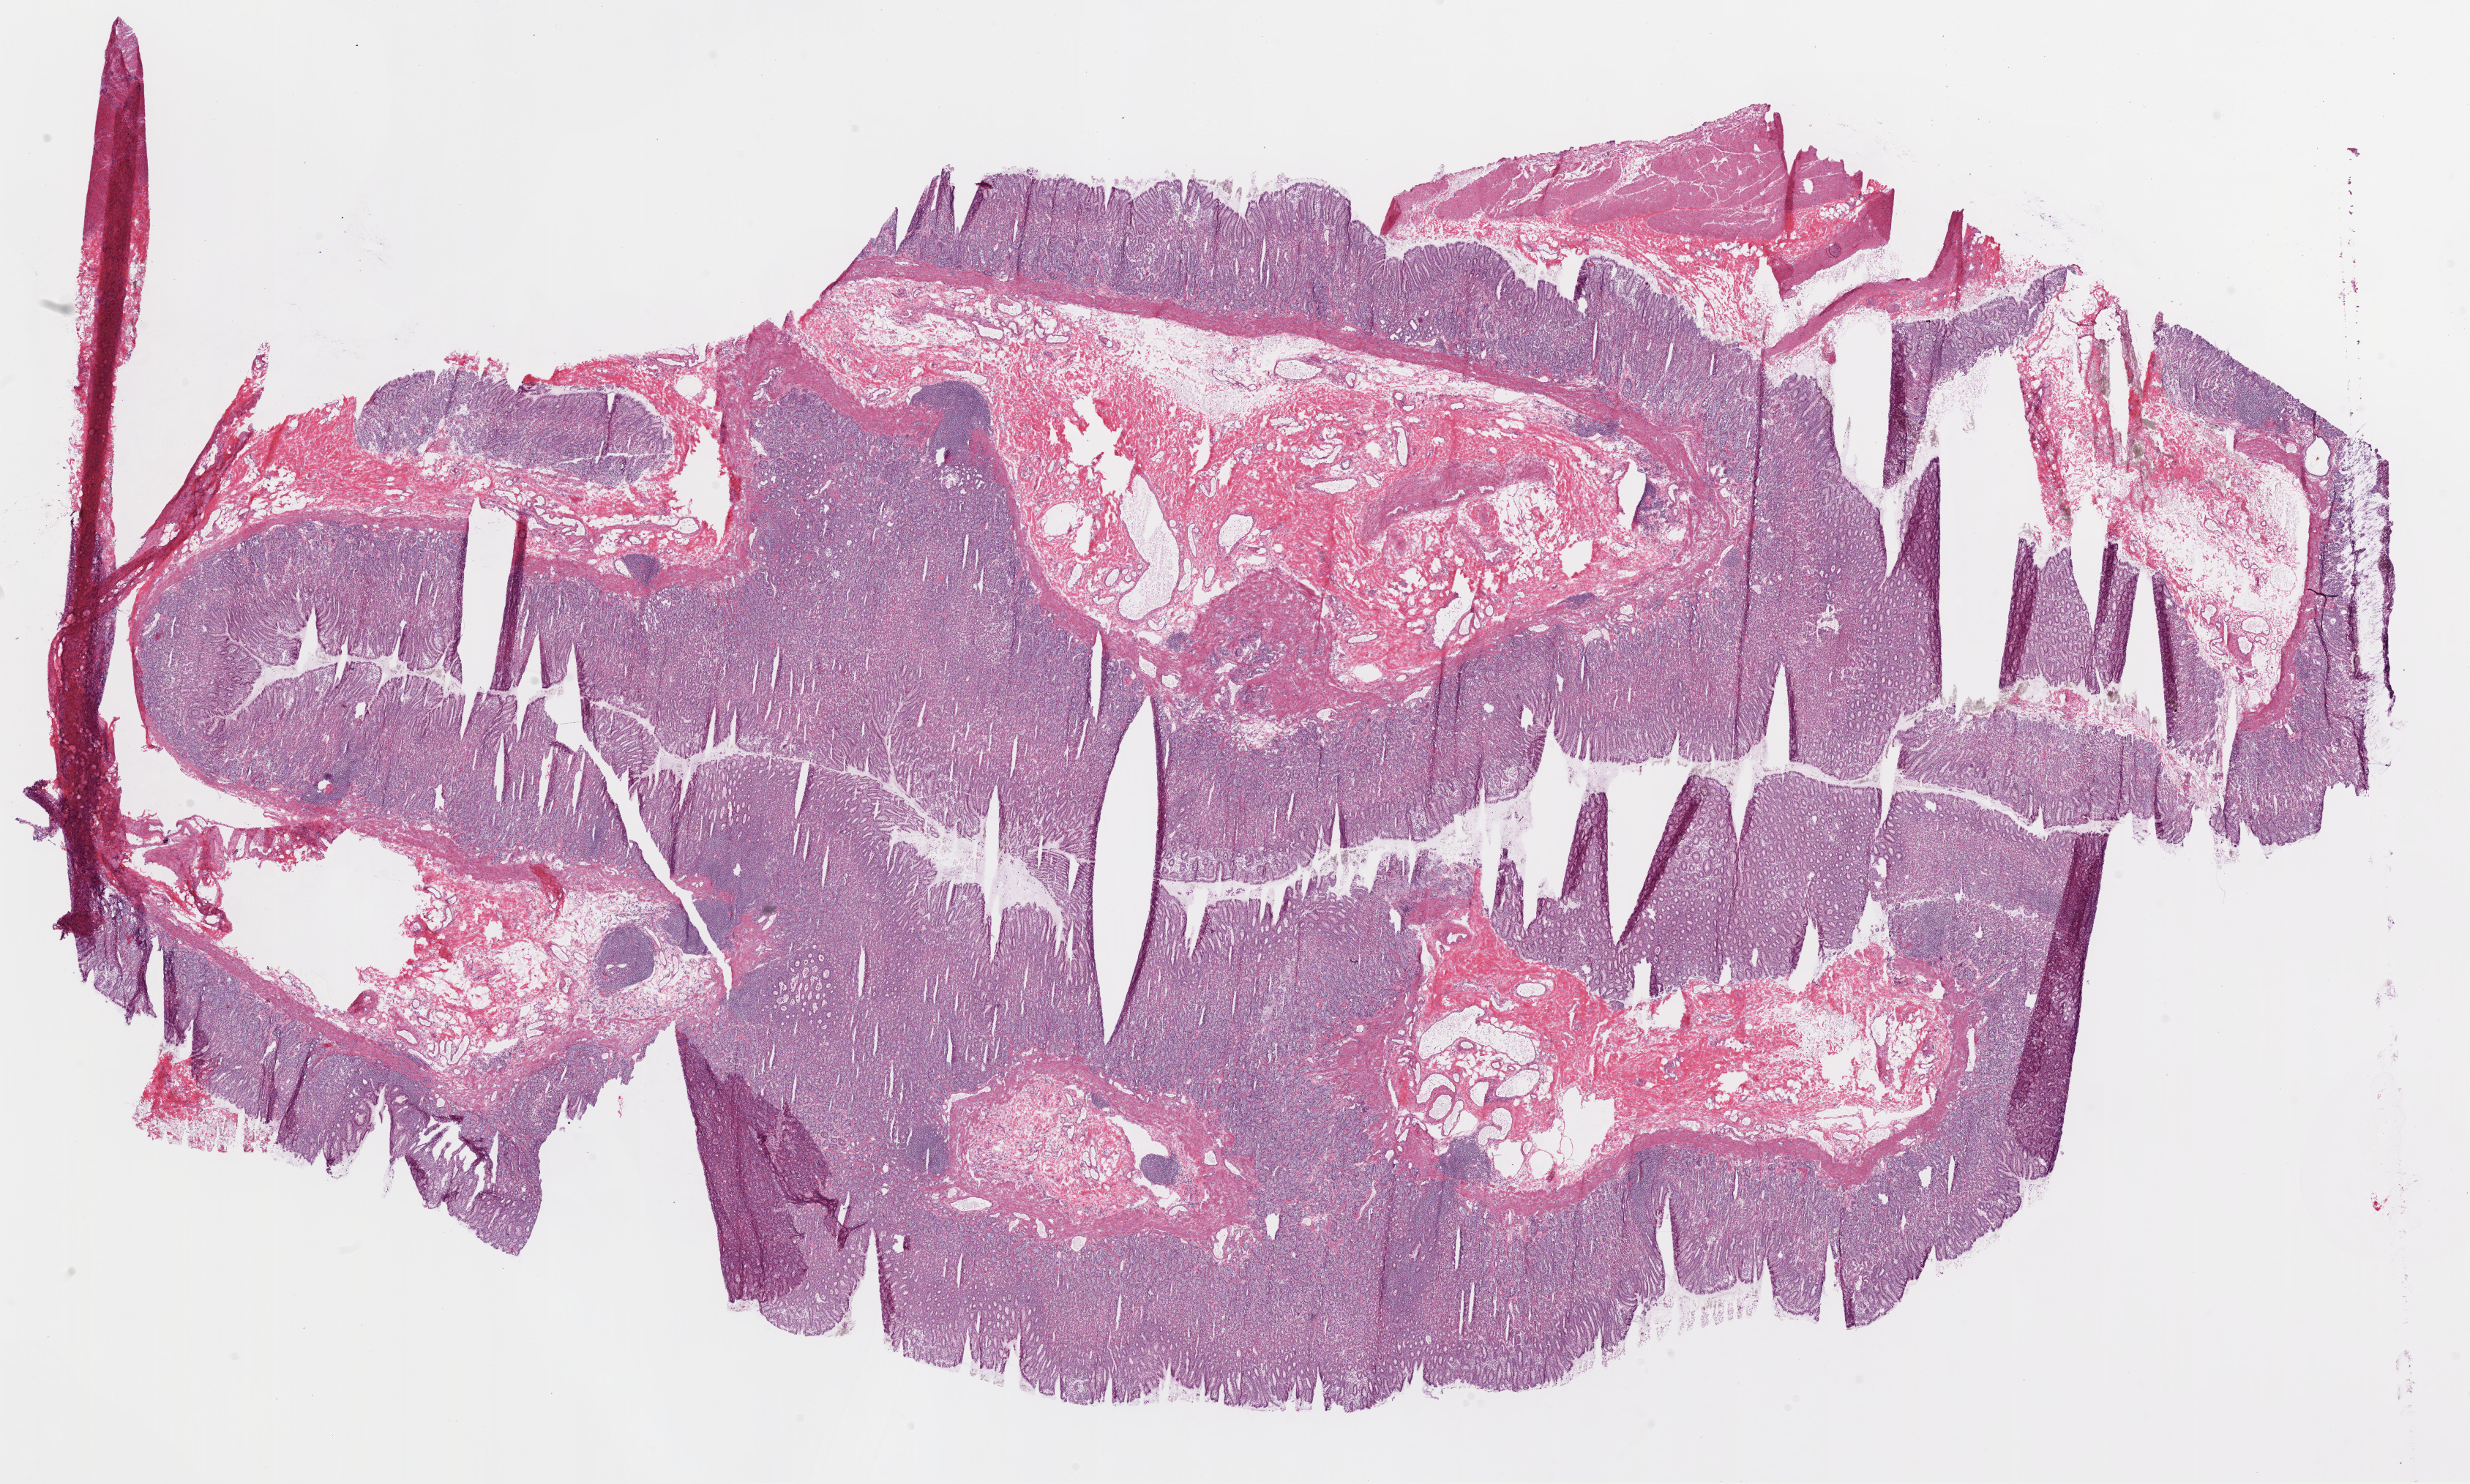
Whole-slide histology image, H&E, a low-resolution overview of the entire scanned area, about 27.1 x 16.3 mm; frozen section; solid tissue normal (non-tumour tissue) sample from the stomach. Patient: male, age at initial diagnosis 56 years.
• this section: solid tissue normal sample (biorepository sample class)
• patient diagnosis: Adenocarcinoma, NOS